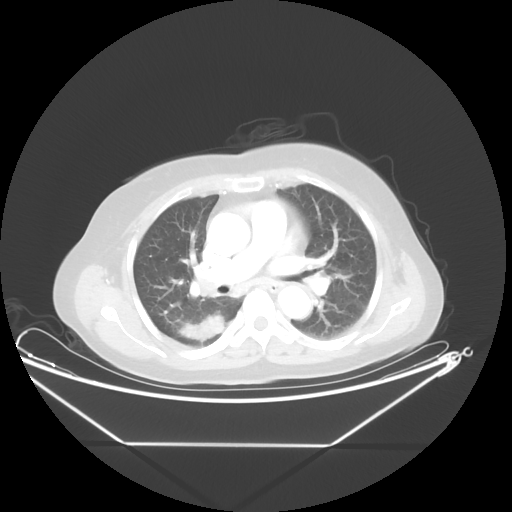
Chest CT, one axial slice. Position 27 of 48 along the scan axis. 100 kVp. Lung window (W 1500 / L -600 HU). 5 mm slice thickness. 512 × 512 image matrix, field of view 462 × 462 mm. Patient: female, 62 years. Case-level facts recorded for this patient, not image findings: clinical TNM (as recorded): T1c N0 M0.
Structures marked on this image (rectangle marked by the reading radiologist):
- lung tumour (recorded histology: adenocarcinoma): bounding box [x1, y1, x2, y2] px = [172, 302, 232, 354]